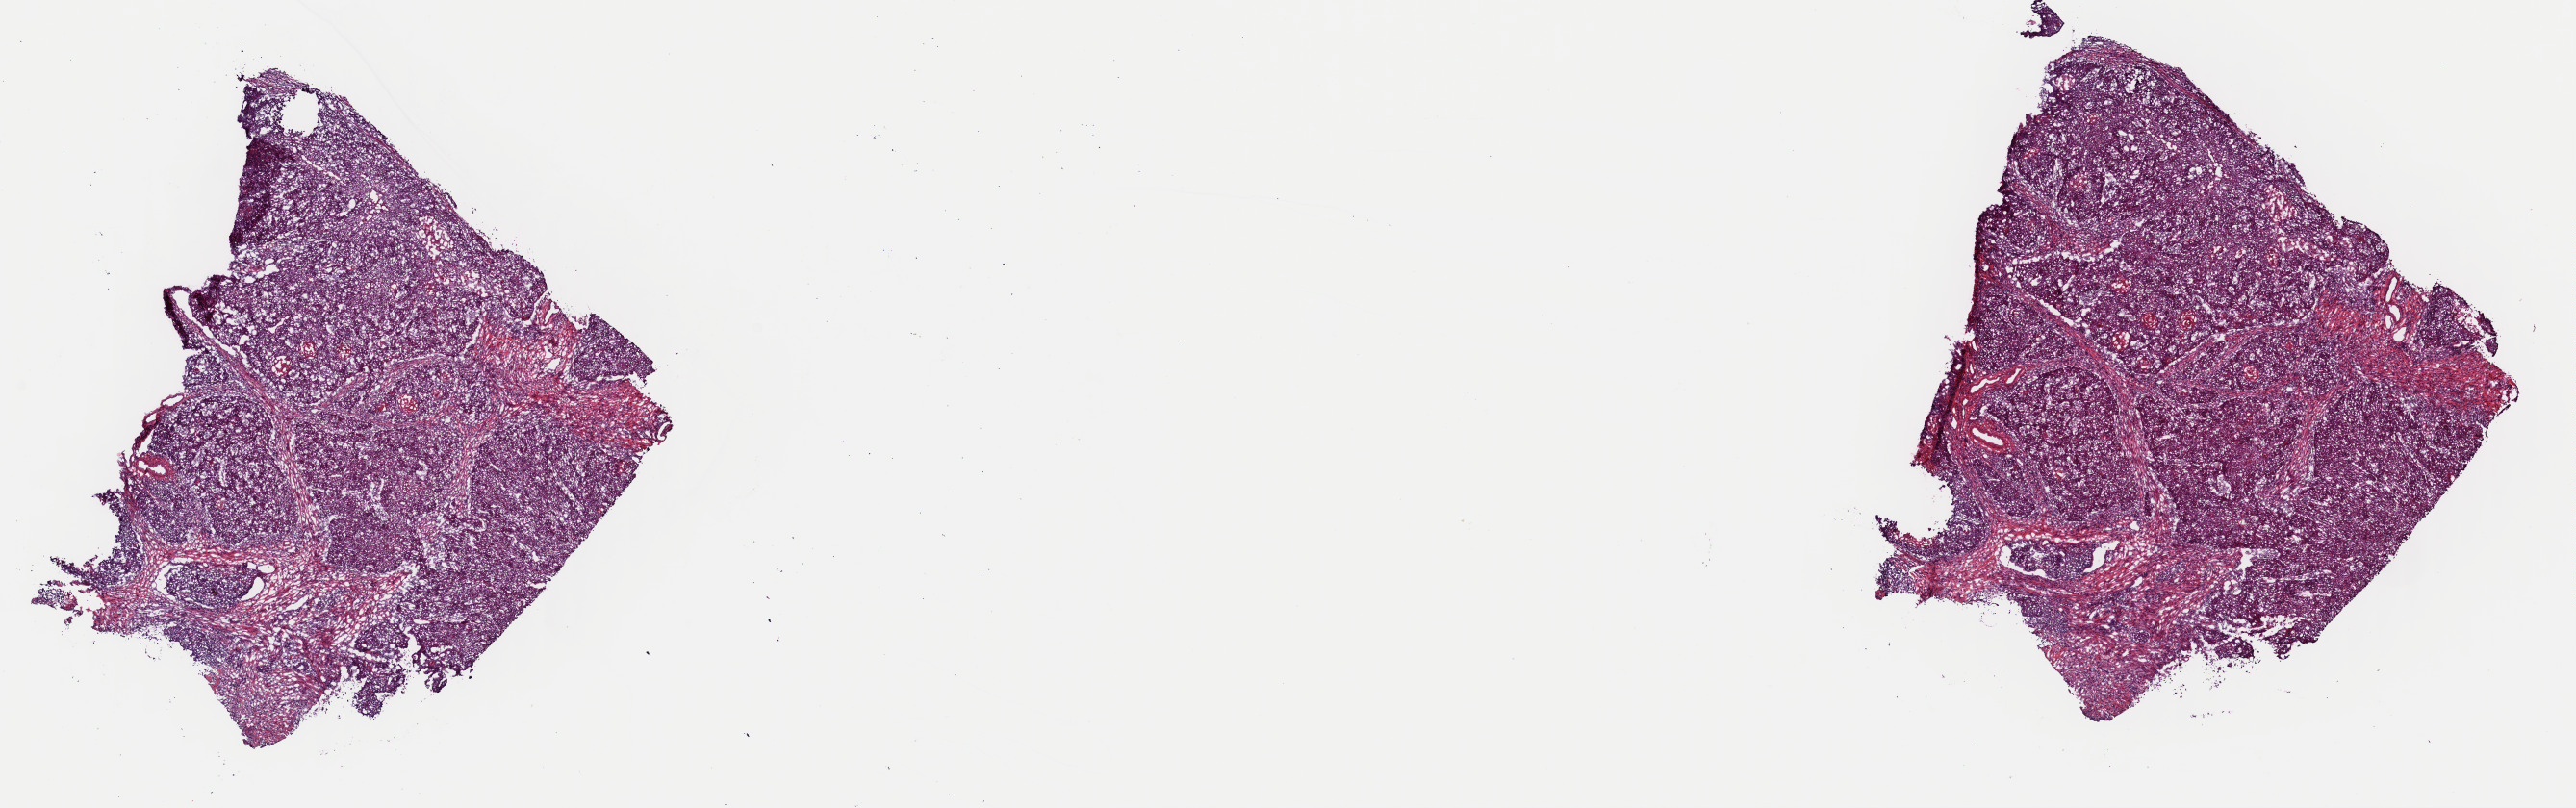
Digitized H&E-stained tissue section (whole slide), whole scanned area (about 21.1 x 6.6 mm) shown as a low-resolution overview, frozen section from the top of the tissue portion, sample: primary tumour, head and neck. Patient: female, age at initial diagnosis 55 years. Histologic grade: G2 (moderately differentiated). Composition of this section per pathologist review: tumour cells 65%, tumour nuclei 80%, normal cells 0%, stromal cells 30%, necrosis 5%. Inflammatory infiltration, as recorded: lymphocyte infiltration 12%, monocyte infiltration 0%, neutrophil infiltration 0%.
AJCC pathologic stage: IVA. Laterality: left. Diagnosis: Squamous cell carcinoma, NOS (tonsil, NOS).